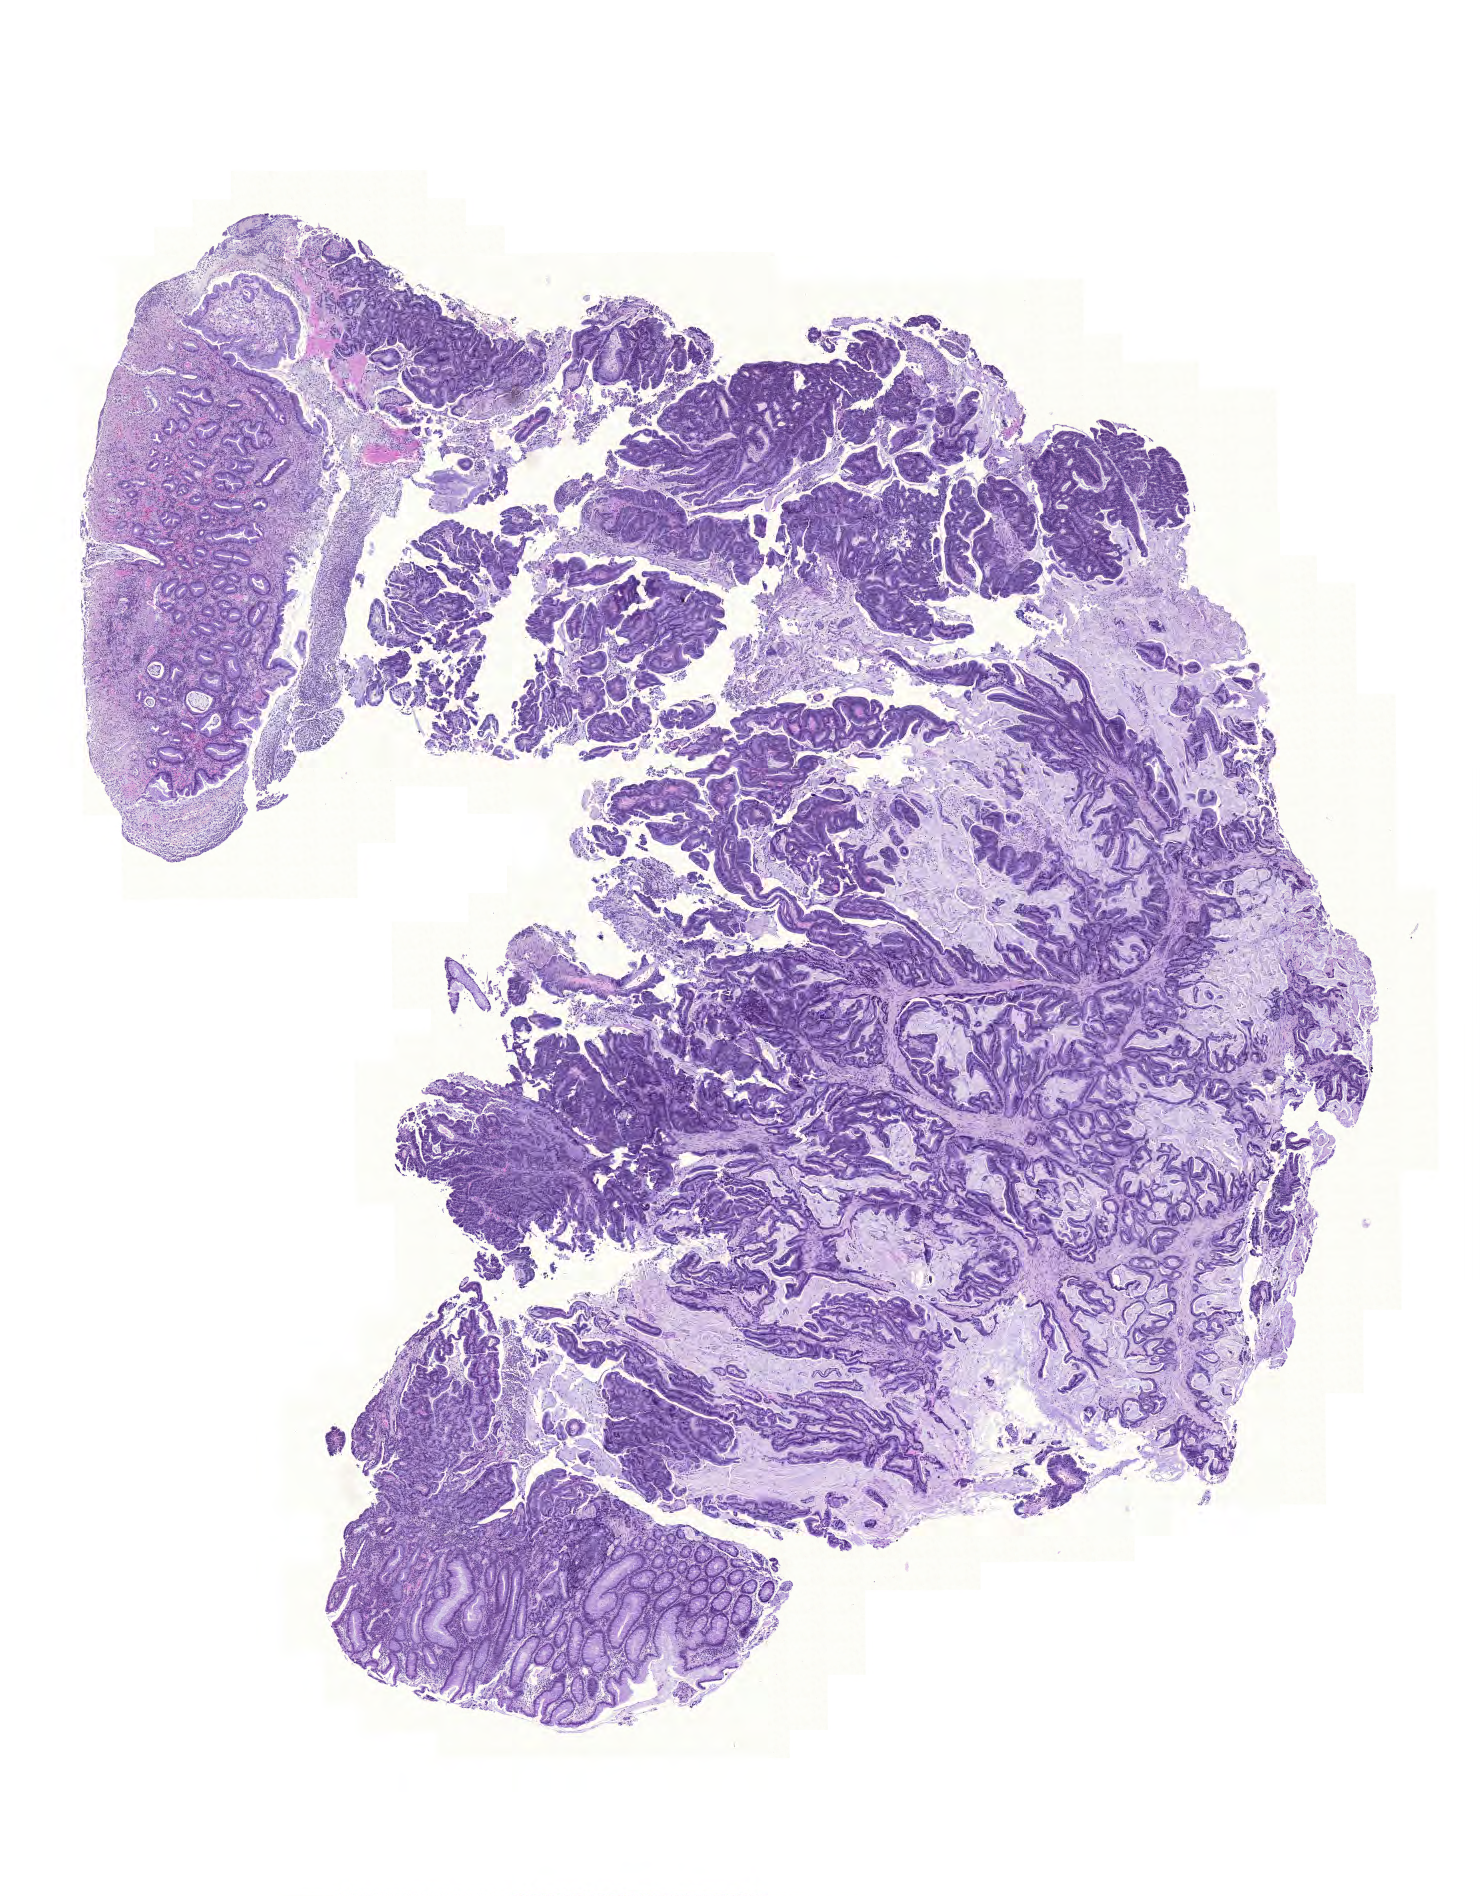
Digitized H&E tissue section (whole slide) — low-resolution overview of the scanned area, about 11.0 x 14.1 mm. Formalin-fixed paraffin-embedded (FFPE) diagnostic section. Colon, primary tumour sample. Patient sex: male.
- pathologic diagnosis: Adenocarcinoma, NOS (ascending colon)
- AJCC pathologic stage: IIIB (6th edition)